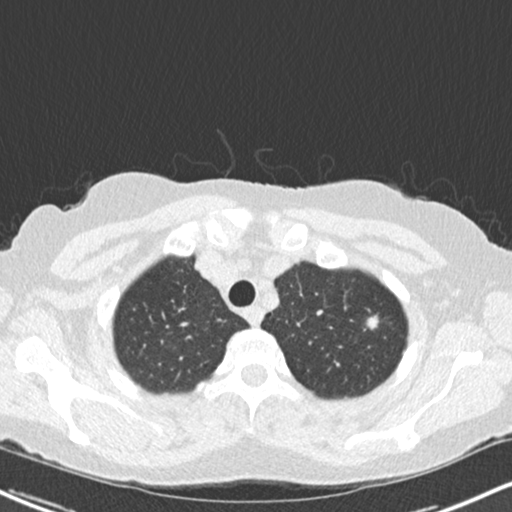
Low-dose screening chest CT, axial slice, first (baseline) screen, lung window (W 1500 / L -600 HU), 2 mm slice thickness, standard (soft-tissue) reconstruction kernel (B30f), slice 24 of 217 in the series, 512 × 512 image matrix, field of view 319 × 319 mm. Female, age 64 years at enrolment. Former smoker at enrolment.
Lesion marked by an expert reader, bounding box [x1, y1, x2, y2] px = [358, 307, 388, 339]. The screening reader recorded 2 non-calcified nodules or masses ≥4 mm on this exam; which of them this box marks is not recorded. Later outcome: lung cancer diagnosed 477 days after this screen (after the second annual screen) — signet ring cell carcinoma, right upper lobe, poorly differentiated (G3), stage IA (AJCC 6th edition), 15 mm at pathology.